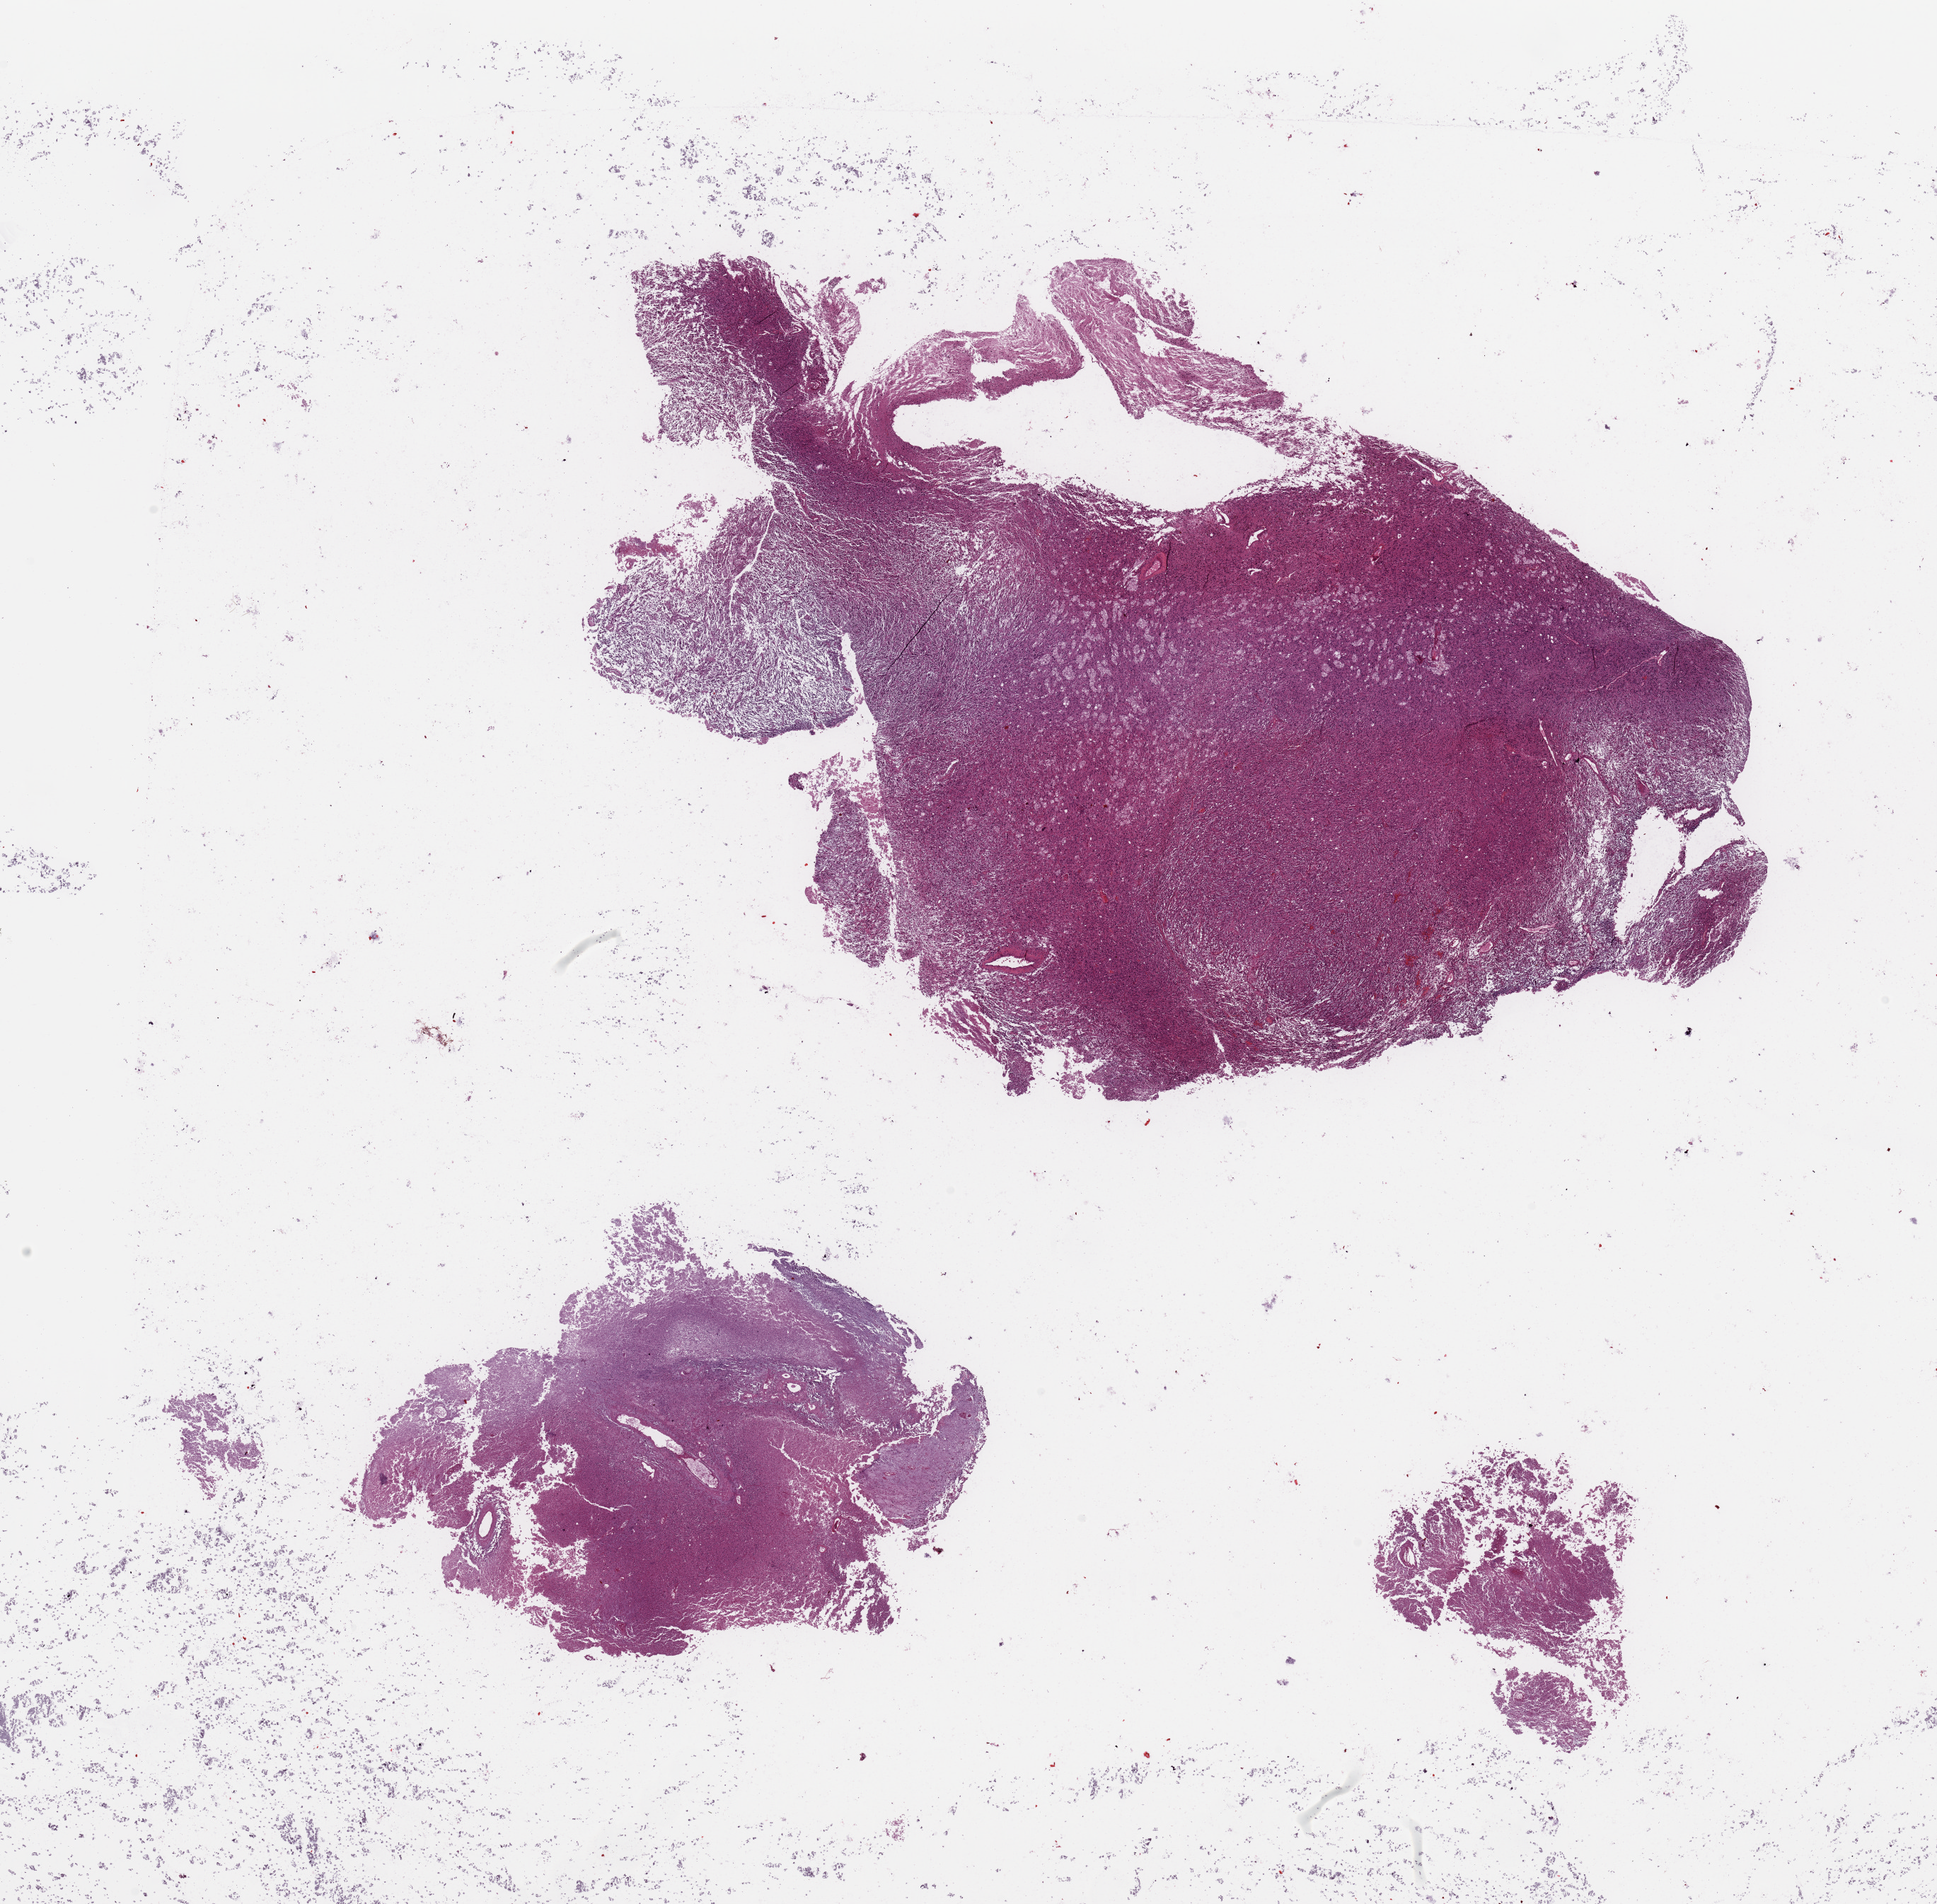
Whole-slide histology image, H&E — a low-resolution overview of the entire scanned area, about 21.7 x 21.3 mm (acquisition: 20x scan). Tumour tissue sample, brain. Patient: female, age 24 years.
Histologic diagnosis: Glioblastoma.